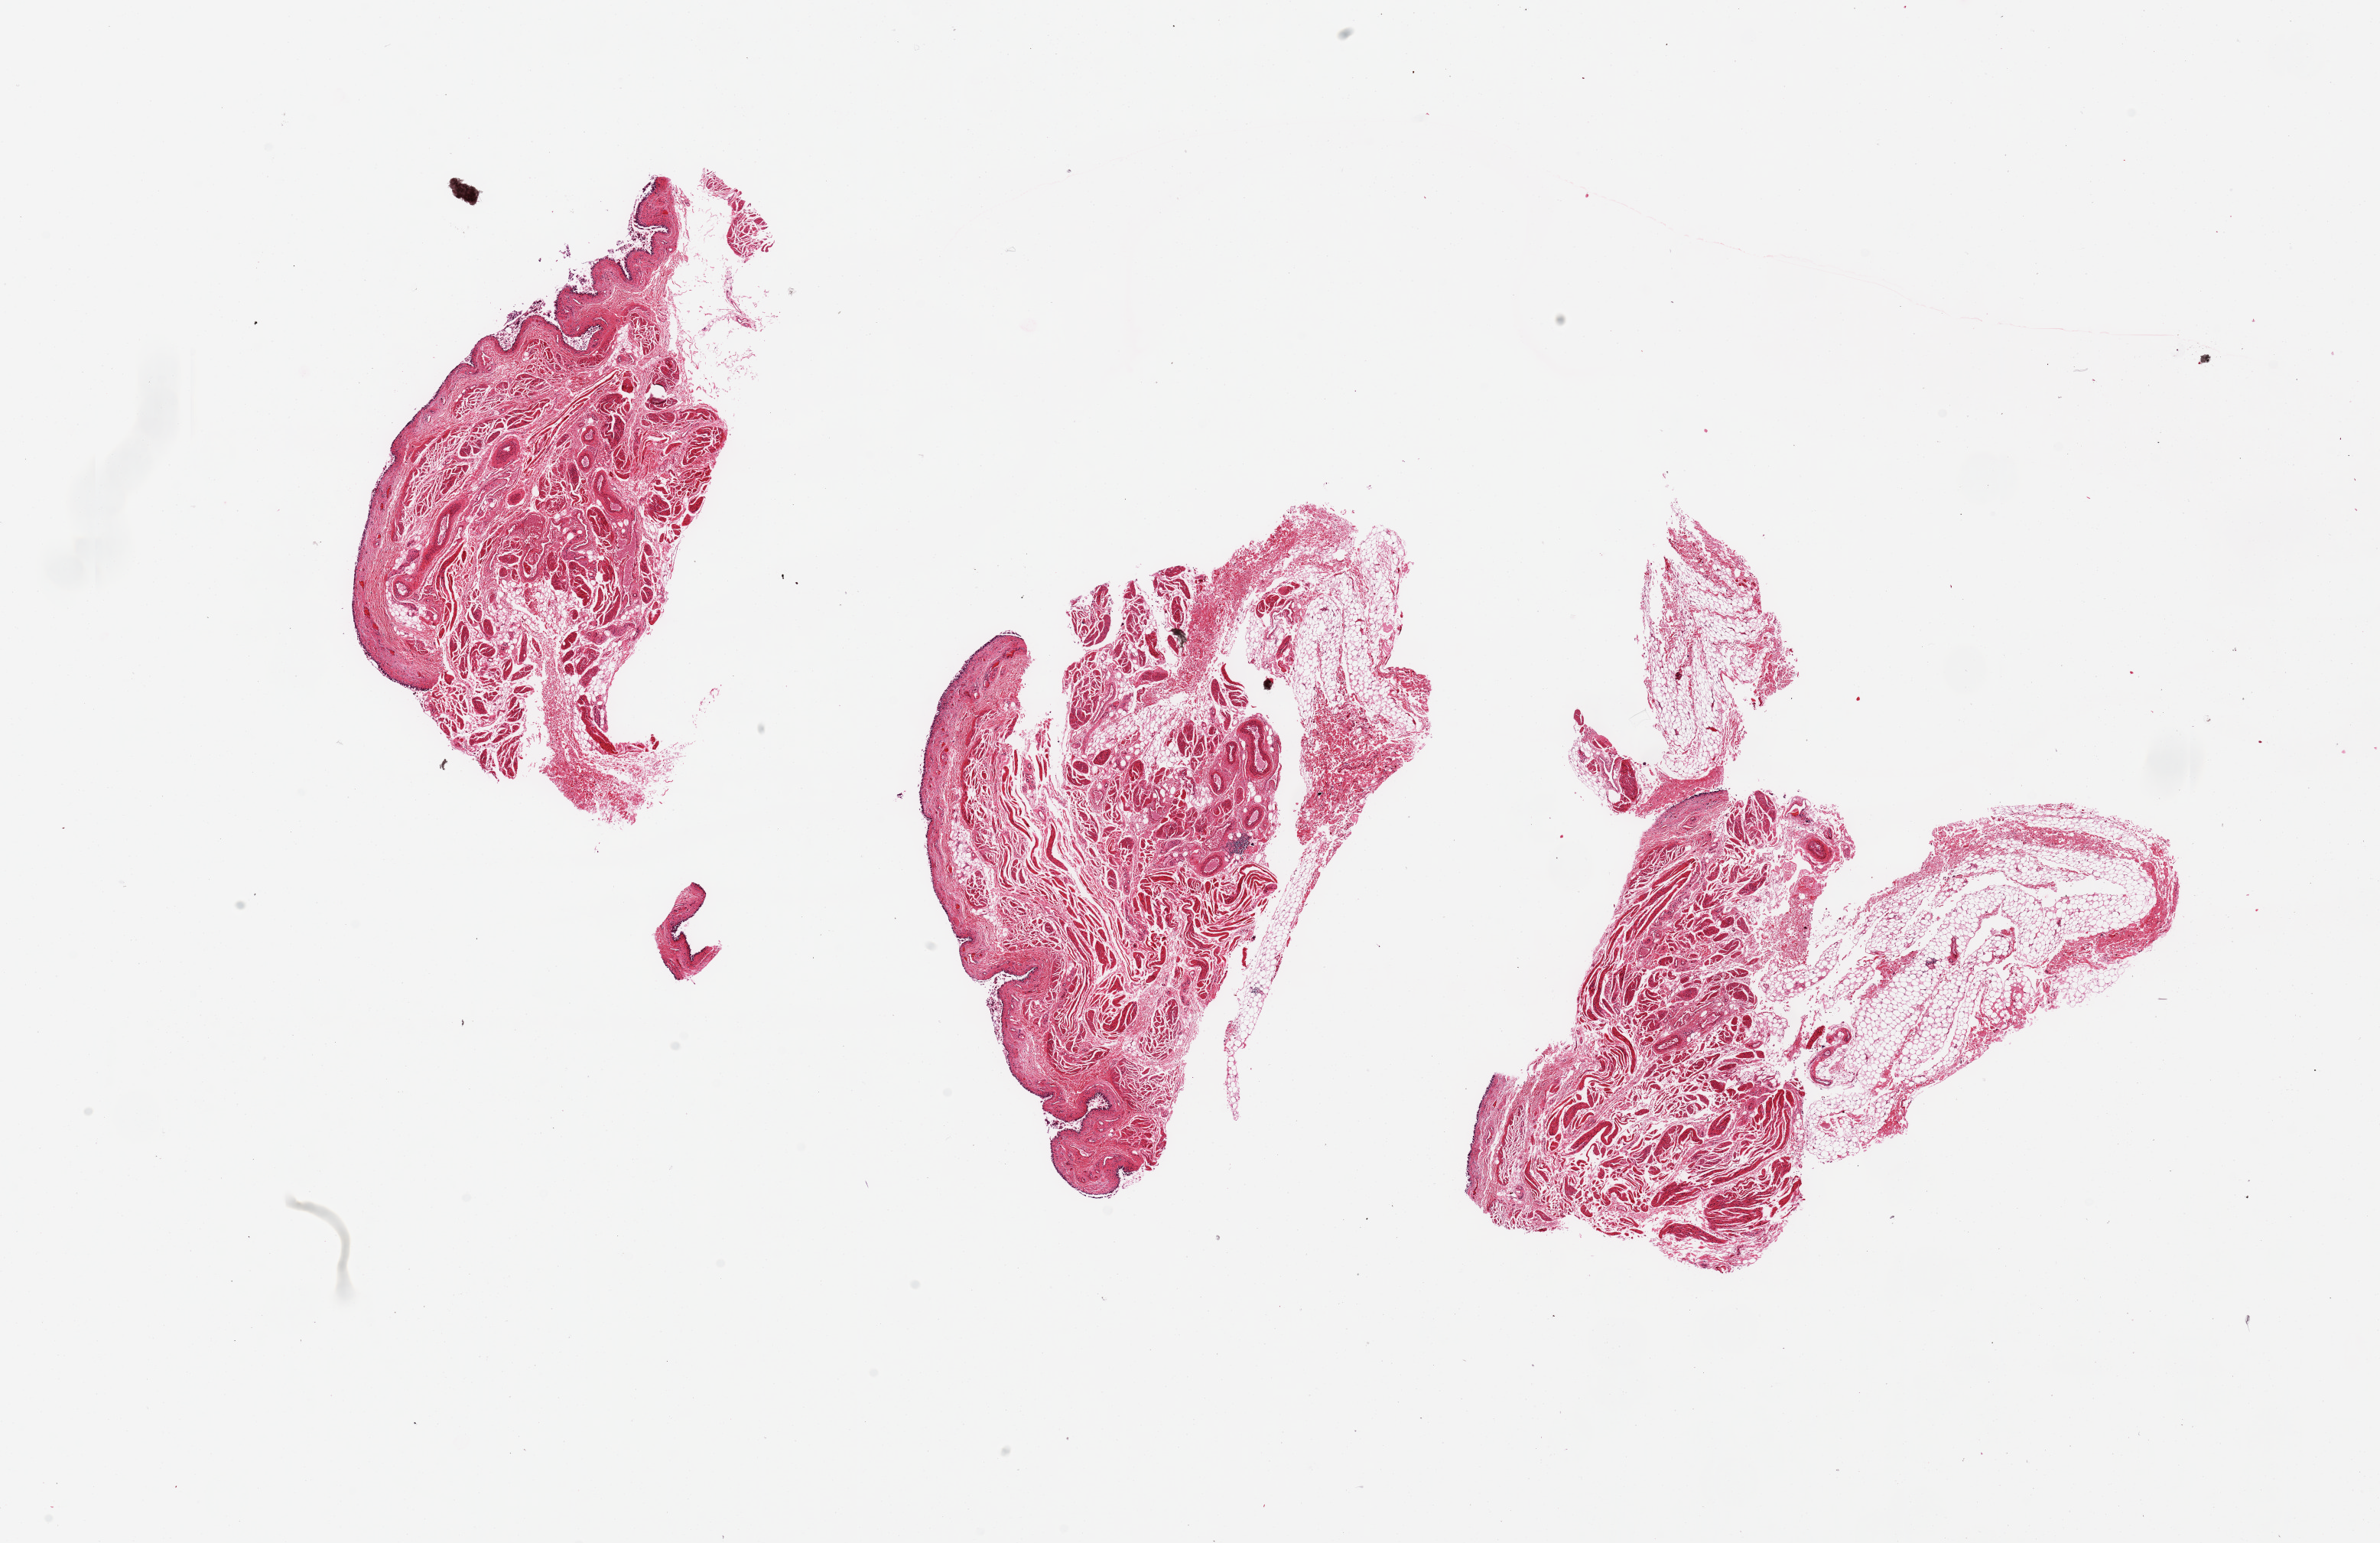
Whole-slide image, H&E stain, brightfield — a low-resolution overview of the entire scanned area, about 24.6 x 16.0 mm (slide scanned at 20x); PAXgene-fixed, paraffin-embedded tissue; sampled site (target tissue): urinary bladder; tissue donor sample. Female donor.
• review note (as recorded): 3 pieces, 4.8x3 mm; Surface sloughed